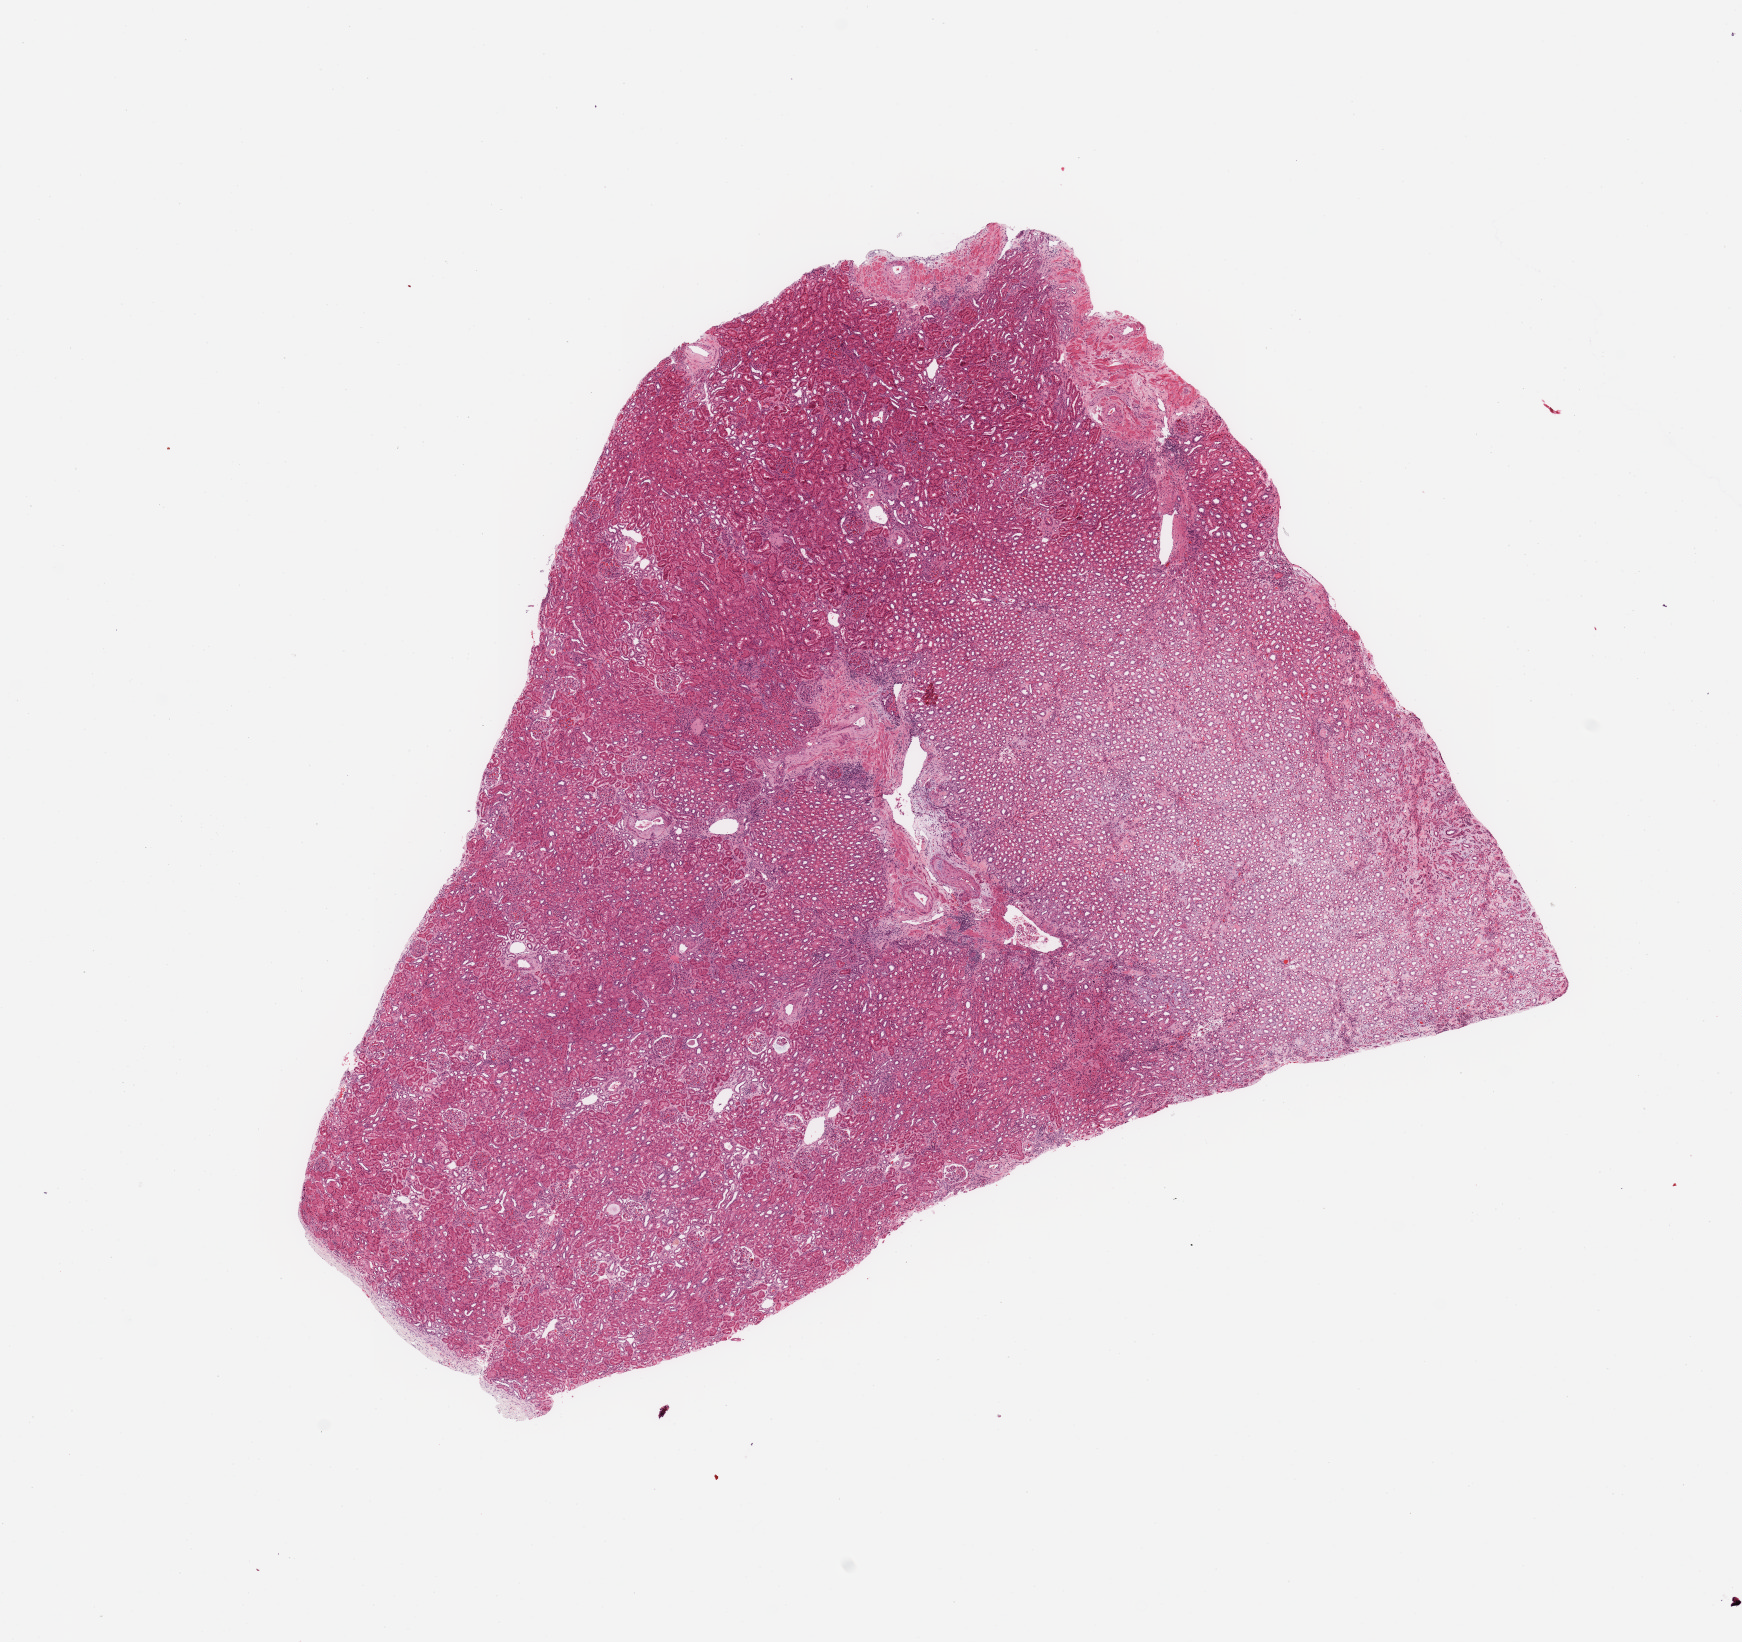
Whole-slide histology image, H&E — low-resolution overview of the scanned area, about 13.8 x 13.0 mm (slide scanned at 20x). Normal (non-tumour) tissue sample, sampled site: kidney. Patient: male, age 63 years.
This section: normal (non-tumour) tissue from the same patient. Patient diagnosis: Renal cell carcinoma, NOS.